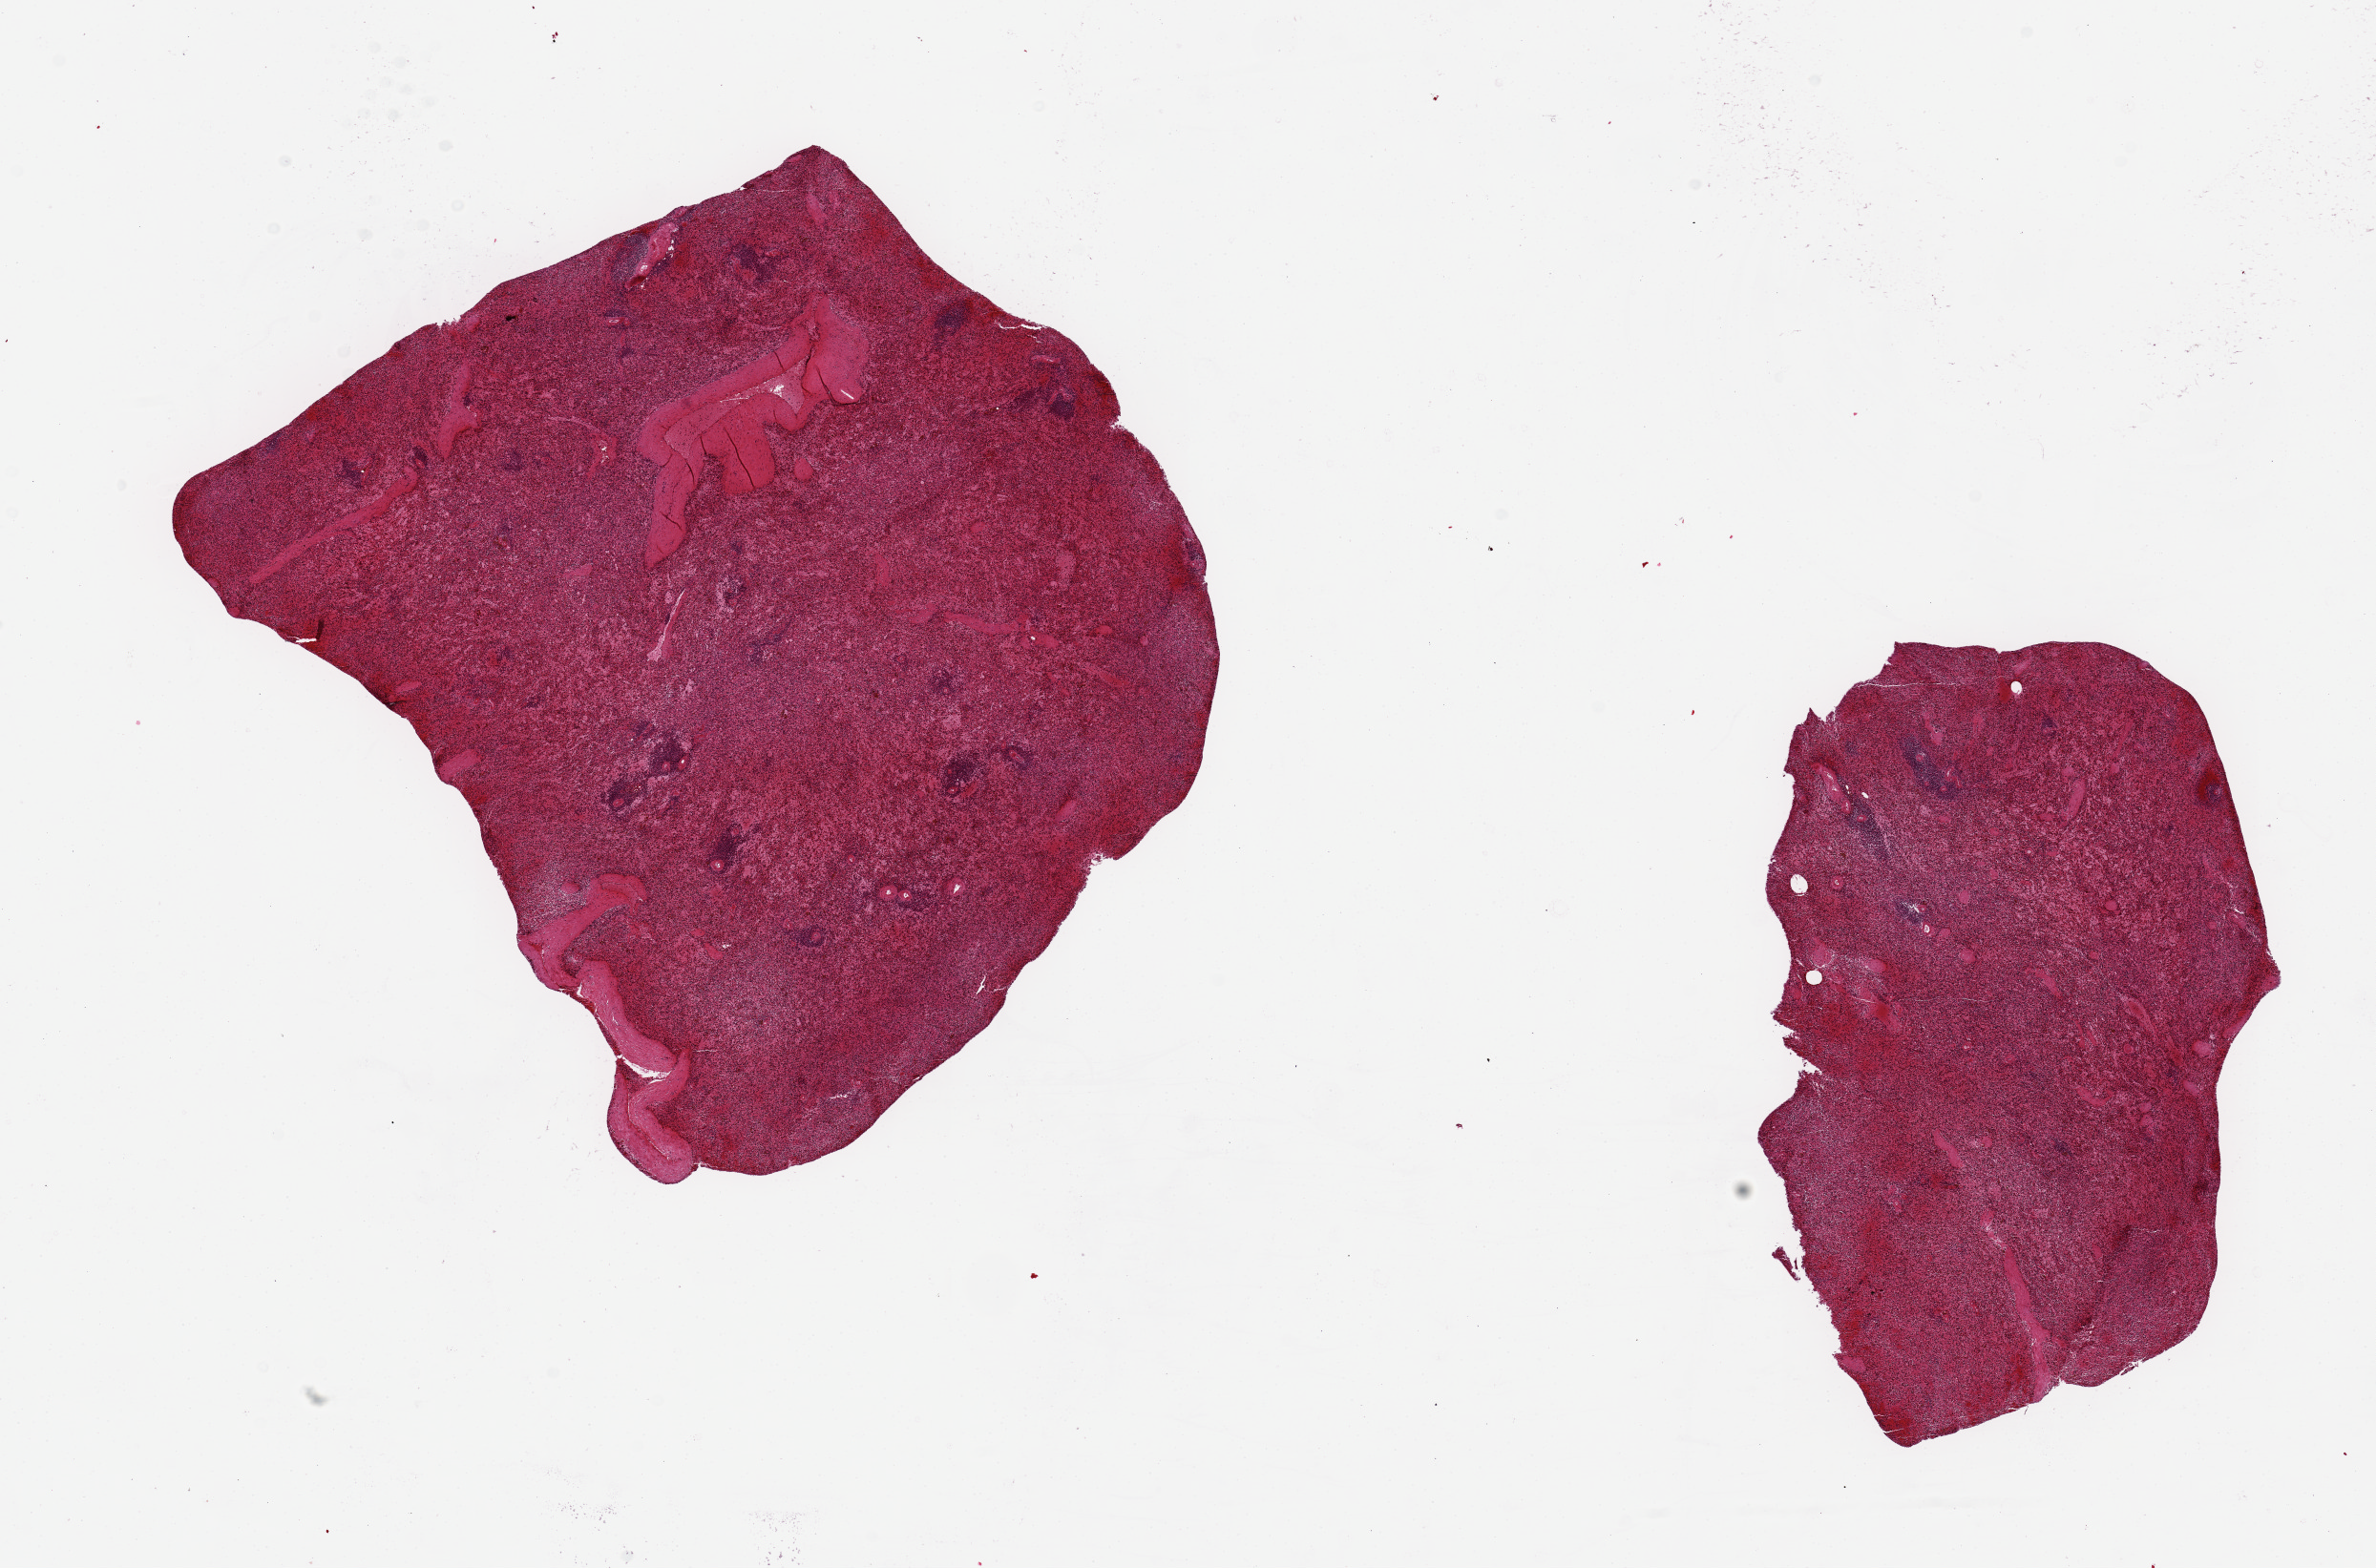
Digitized hematoxylin and eosin (H&E)-stained section — a low-resolution overview of the entire scanned area, about 19.7 x 13.0 mm, PAXgene-fixed, paraffin-embedded tissue, target tissue: spleen, donor tissue sample.
- pathologist's review note for this sample: 2 pieces ~7x5mm